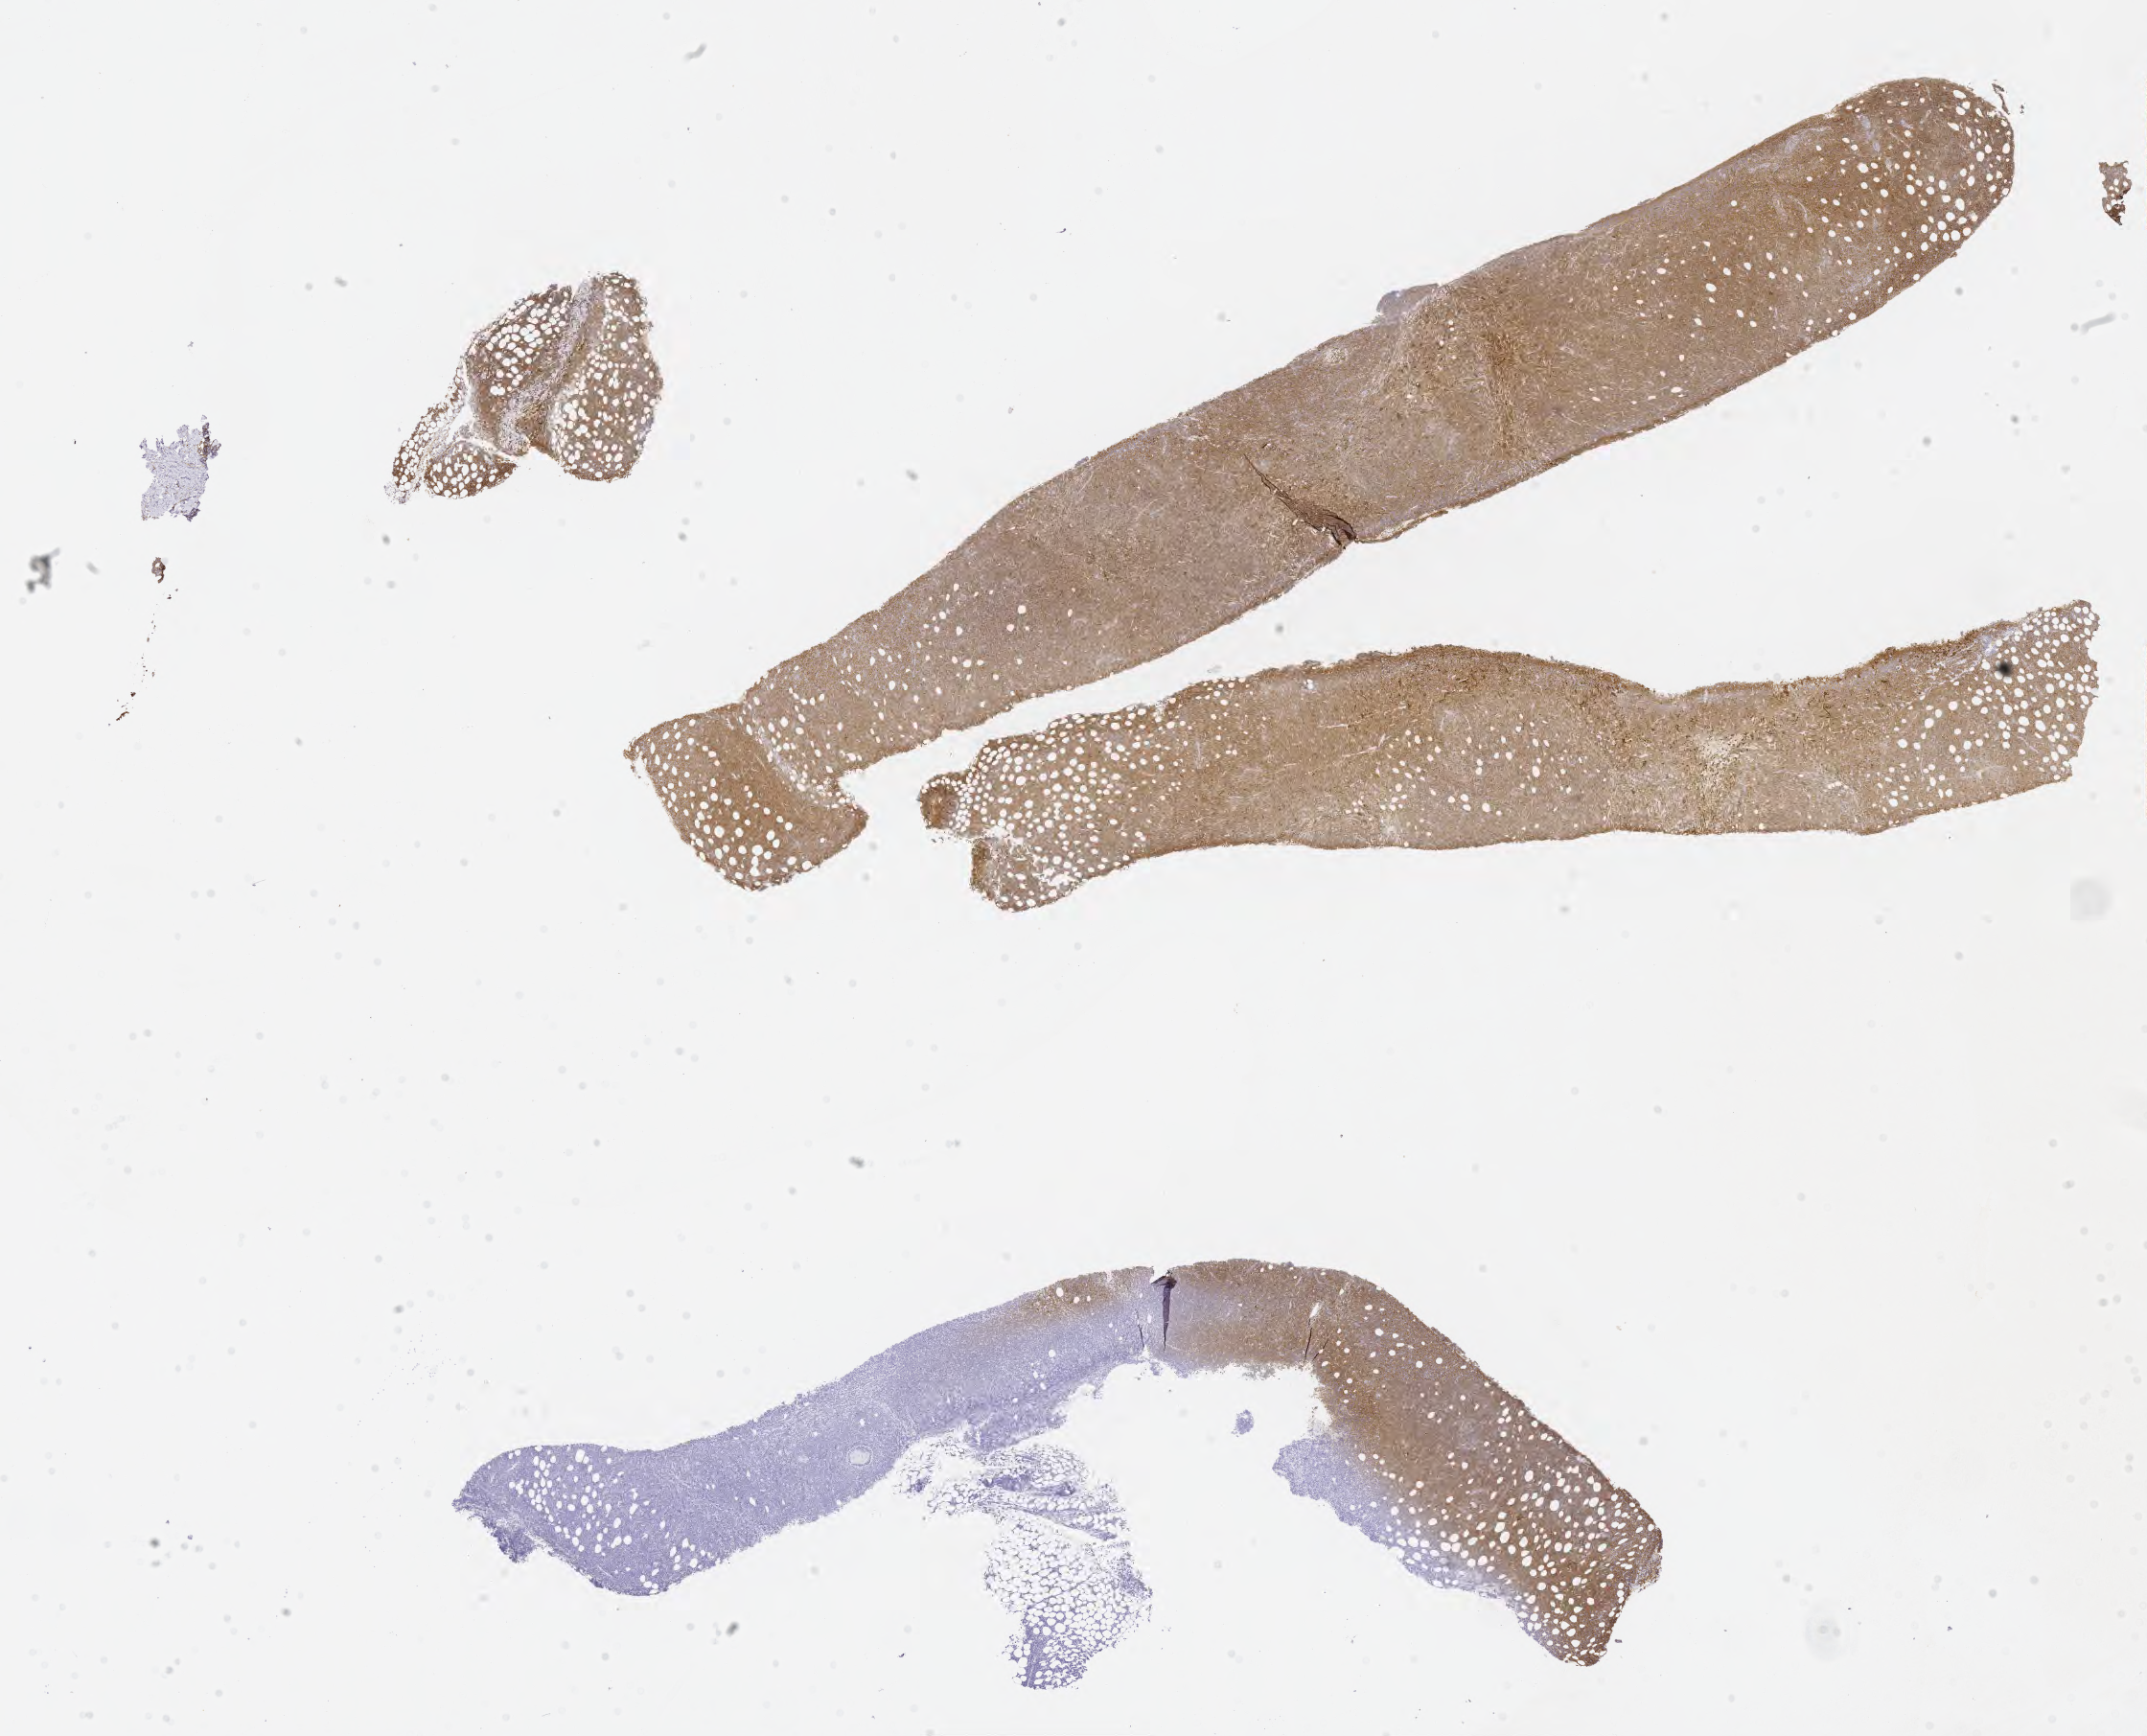
Immunohistochemistry (IHC) whole-slide image stained for CD10 — a low-resolution overview of the entire scanned area, about 18.1 x 14.6 mm, tumor tissue. Patient: female, 43 years old.
• diagnosis: Burkitt lymphoma, NOS